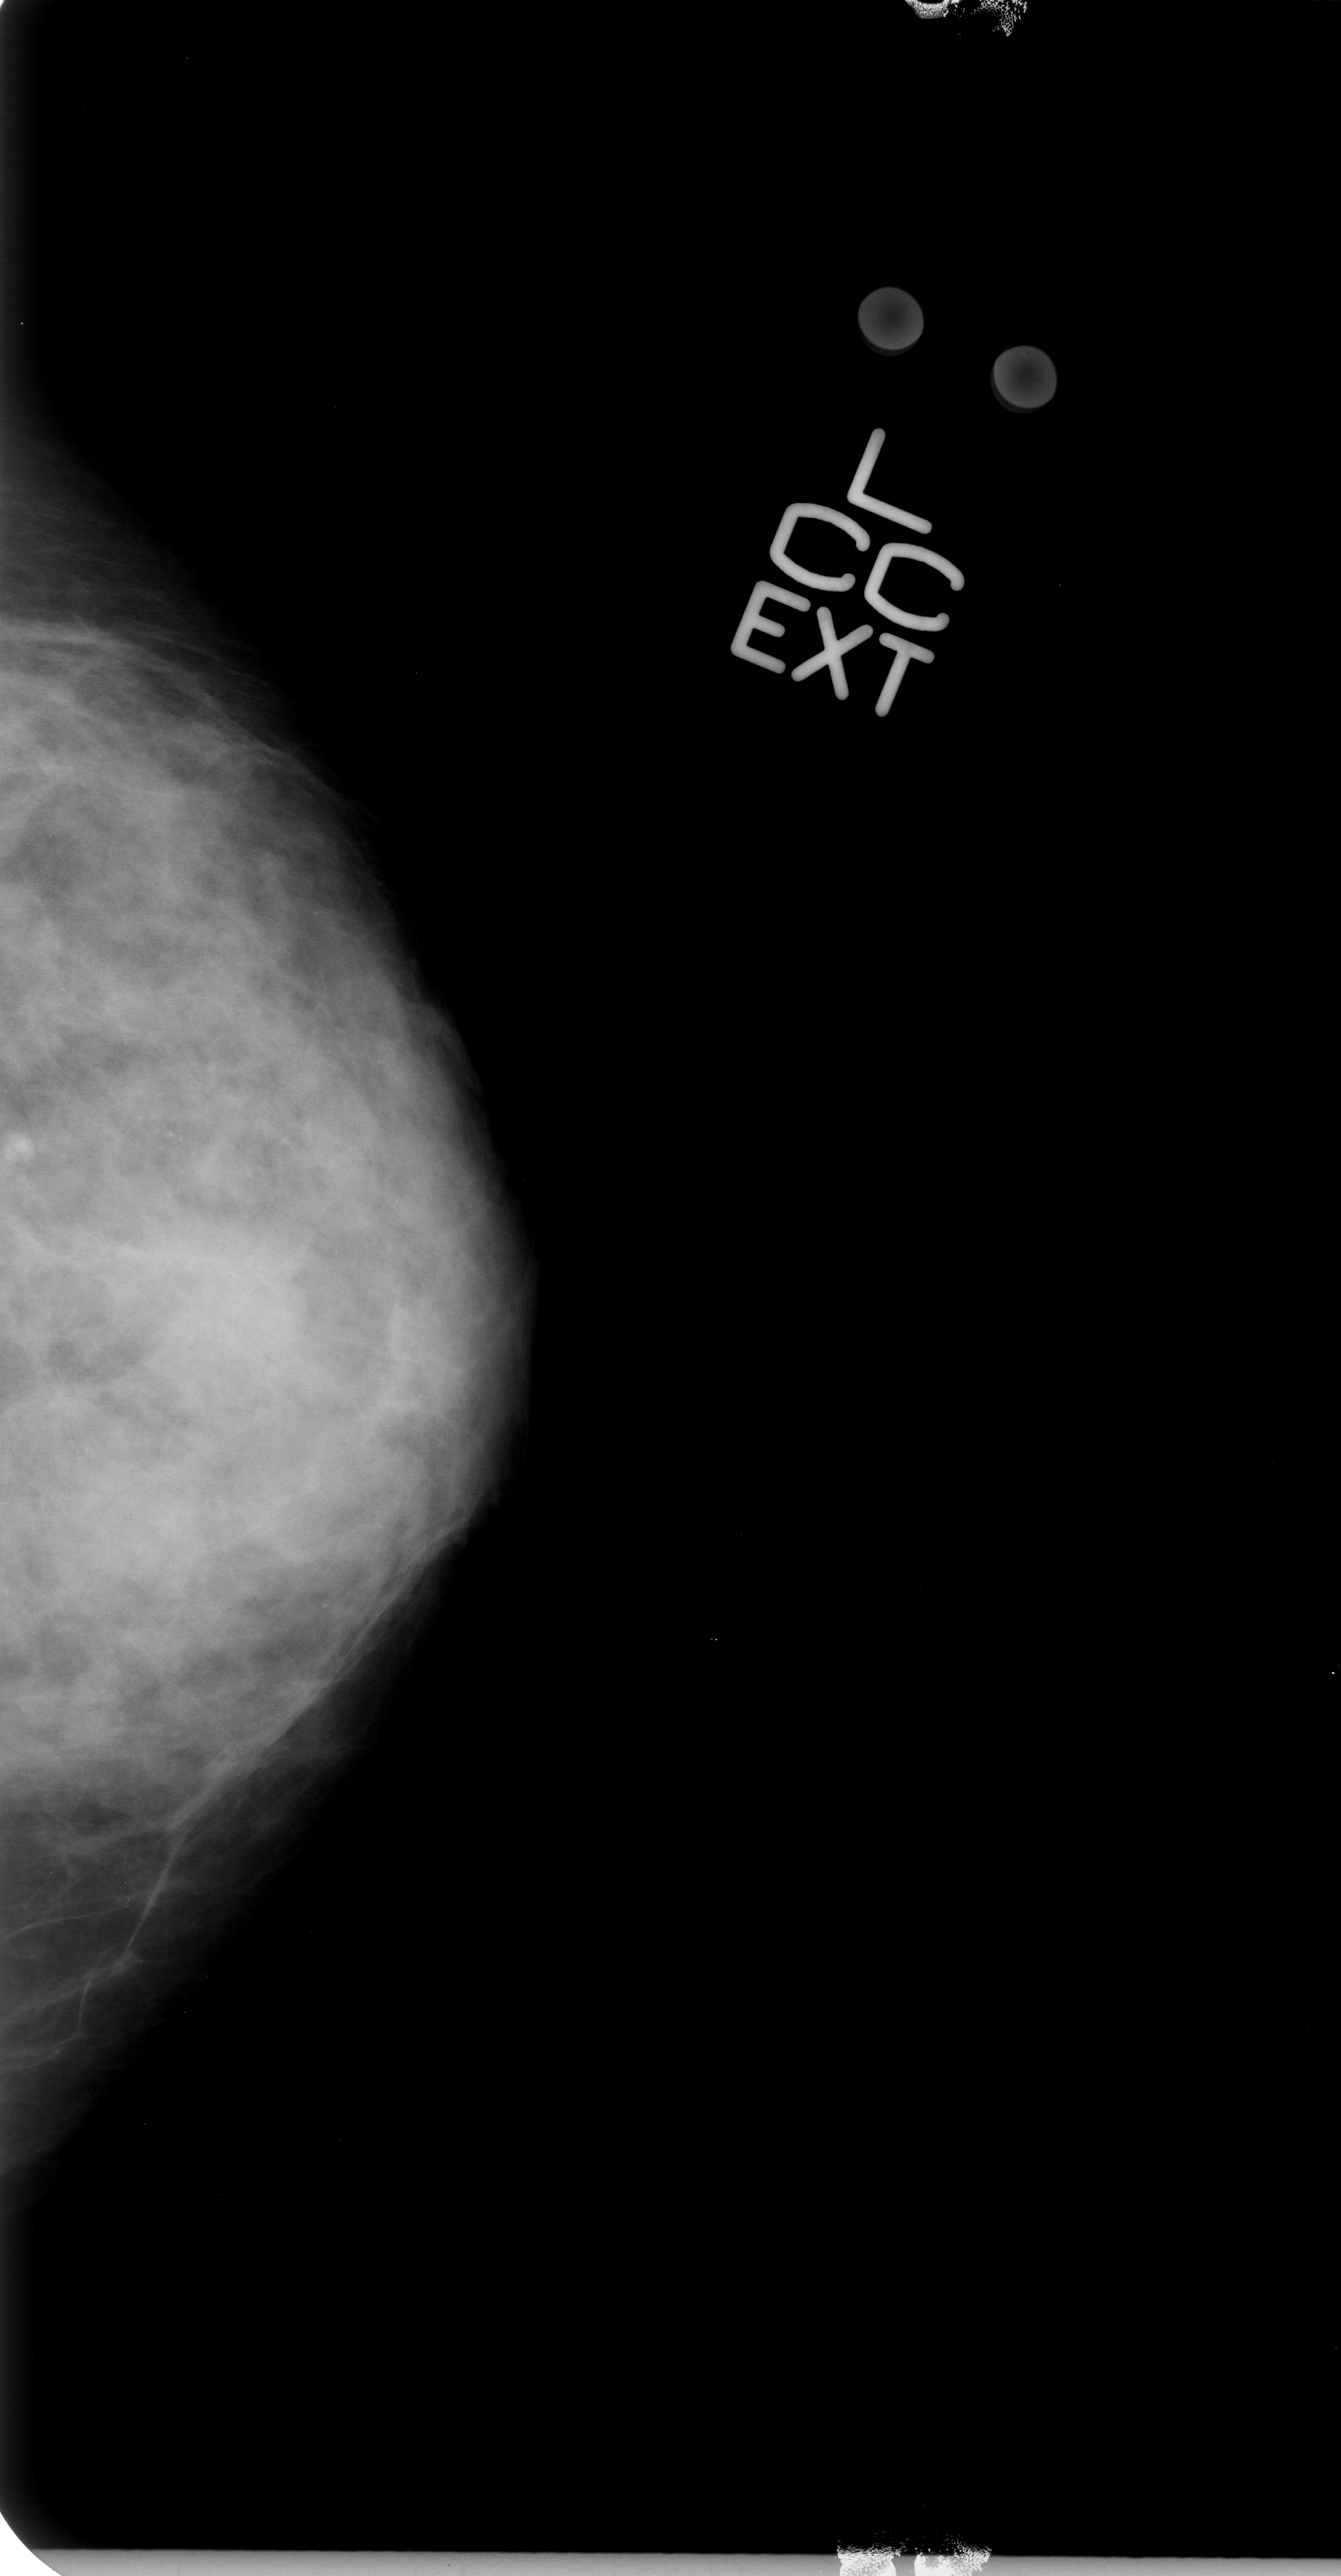
Mammogram (digitized film); left breast; CC view; BI-RADS breast density category 4 (scale 1–4); 1341 × 2576 image matrix.
Expert-marked regions of interest on this film, with their recorded descriptors:
- mass, shape lobulated / architectural distortion, margins obscured / ill defined; BI-RADS assessment category 4; subtlety rating 2 on a 1 (subtle) to 5 (obvious) scale; pathology result (as recorded, not read from the image): malignant: bounding box [x1, y1, x2, y2] px = [142, 1218, 286, 1384]